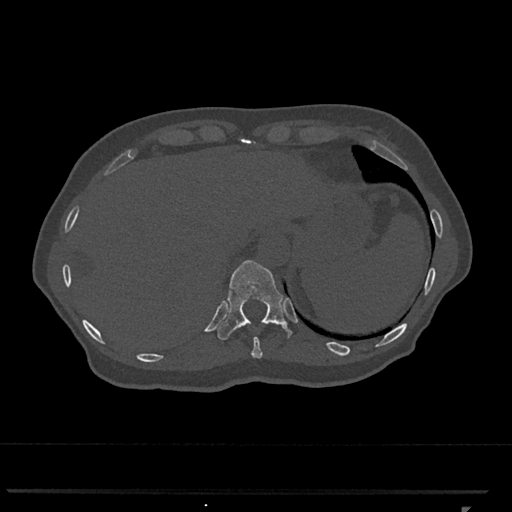
CT including the spine, one axial slice; position 533 of 793 along the scan axis; reconstruction kernel Br40s/3; 120 kVp; bone window (W 1800 / L 400 HU); 0.5 mm slice thickness; 512 × 512 image matrix. Female patient, age 62 years. Case-level facts recorded for this patient, not image findings: primary cancer: renal.
Structures marked on this image (semi-automatically segmented with operator editing):
- T10 vertebra: bounding box [x1, y1, x2, y2] px = [238, 327, 263, 358]
- T11 vertebra: [216, 260, 293, 340]